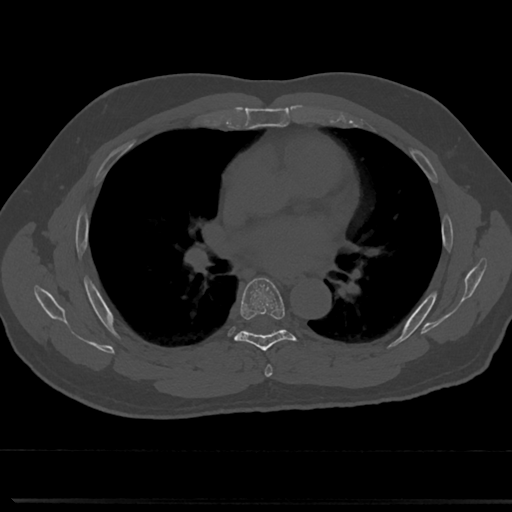
CT including the spine, one axial slice; position 452 of 817 along the scan axis; 120 kVp; bone window (W 1800 / L 400 HU); 0.5 mm slice thickness; 512 × 512 image matrix. Patient: male, 61 years. From the clinical record (not read from this slice): primary cancer: prostate.
Annotated regions visible in this slice (semi-automatically segmented with operator editing):
- T5 vertebra: bounding box [x1, y1, x2, y2] px = [263, 347, 273, 374]
- T6 vertebra: [218, 277, 311, 355]